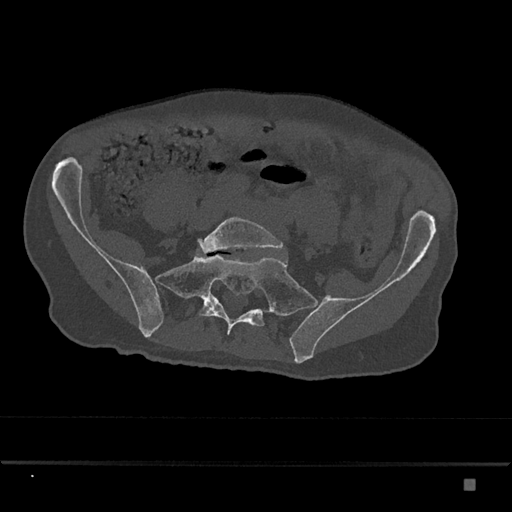
CT including the spine, one axial slice; position 231 of 797 along the scan axis; reconstruction kernel Br40s/3; 120 kVp; bone window (W 1800 / L 400 HU); 0.5 mm slice thickness; 512 × 512 image matrix, field of view 390 × 390 mm. Patient: male, 72 years. From the clinical record (not read from this slice): primary cancer: prostate.
Annotated regions visible in this slice (semi-automatically segmented with operator editing):
- L5 vertebra: box from (x=197, y=217) to (x=284, y=253) px